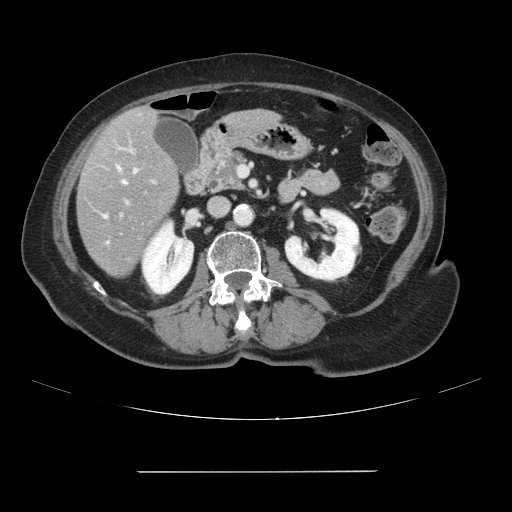
Contrast-enhanced abdominal CT, one axial slice; slice 32 of 111 in the series (ordered by position); 120 kVp; intravenous contrast given; soft-tissue window (W 400 / L 40 HU); 2.5 mm slice thickness; 512 × 512 image matrix, field of view 400 × 400 mm. Female patient, age 74 years. Case-level facts recorded for this patient, not image findings: diagnosis: colorectal cancer liver metastases, imaged before liver resection; multiple liver metastases: yes; largest metastasis: 1.1 cm; disease in both lobes: yes.
Outlined on this slice (expert manual segmentation):
- hepatic veins: box from (x=118, y=168) to (x=125, y=184) px
- liver: (x=78, y=107)–(x=265, y=277)
- planned liver remnant (the part of the liver to remain after resection): (x=141, y=107)–(x=252, y=125)